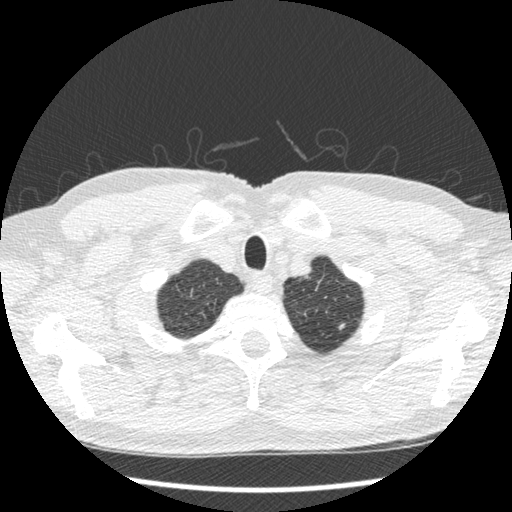
Low-dose screening chest CT, one axial slice; position 411 of 439 along the scan axis; reconstruction kernel STANDARD; lung window (W 1500 / L -600 HU); 1.25 mm slice thickness; 512 × 512 image matrix.
Annotated regions visible in this slice (manually delineated by an expert):
- lesion 1 (nodule, upper lobe of left lung): bounding box [x1, y1, x2, y2] px = [338, 323, 346, 330]